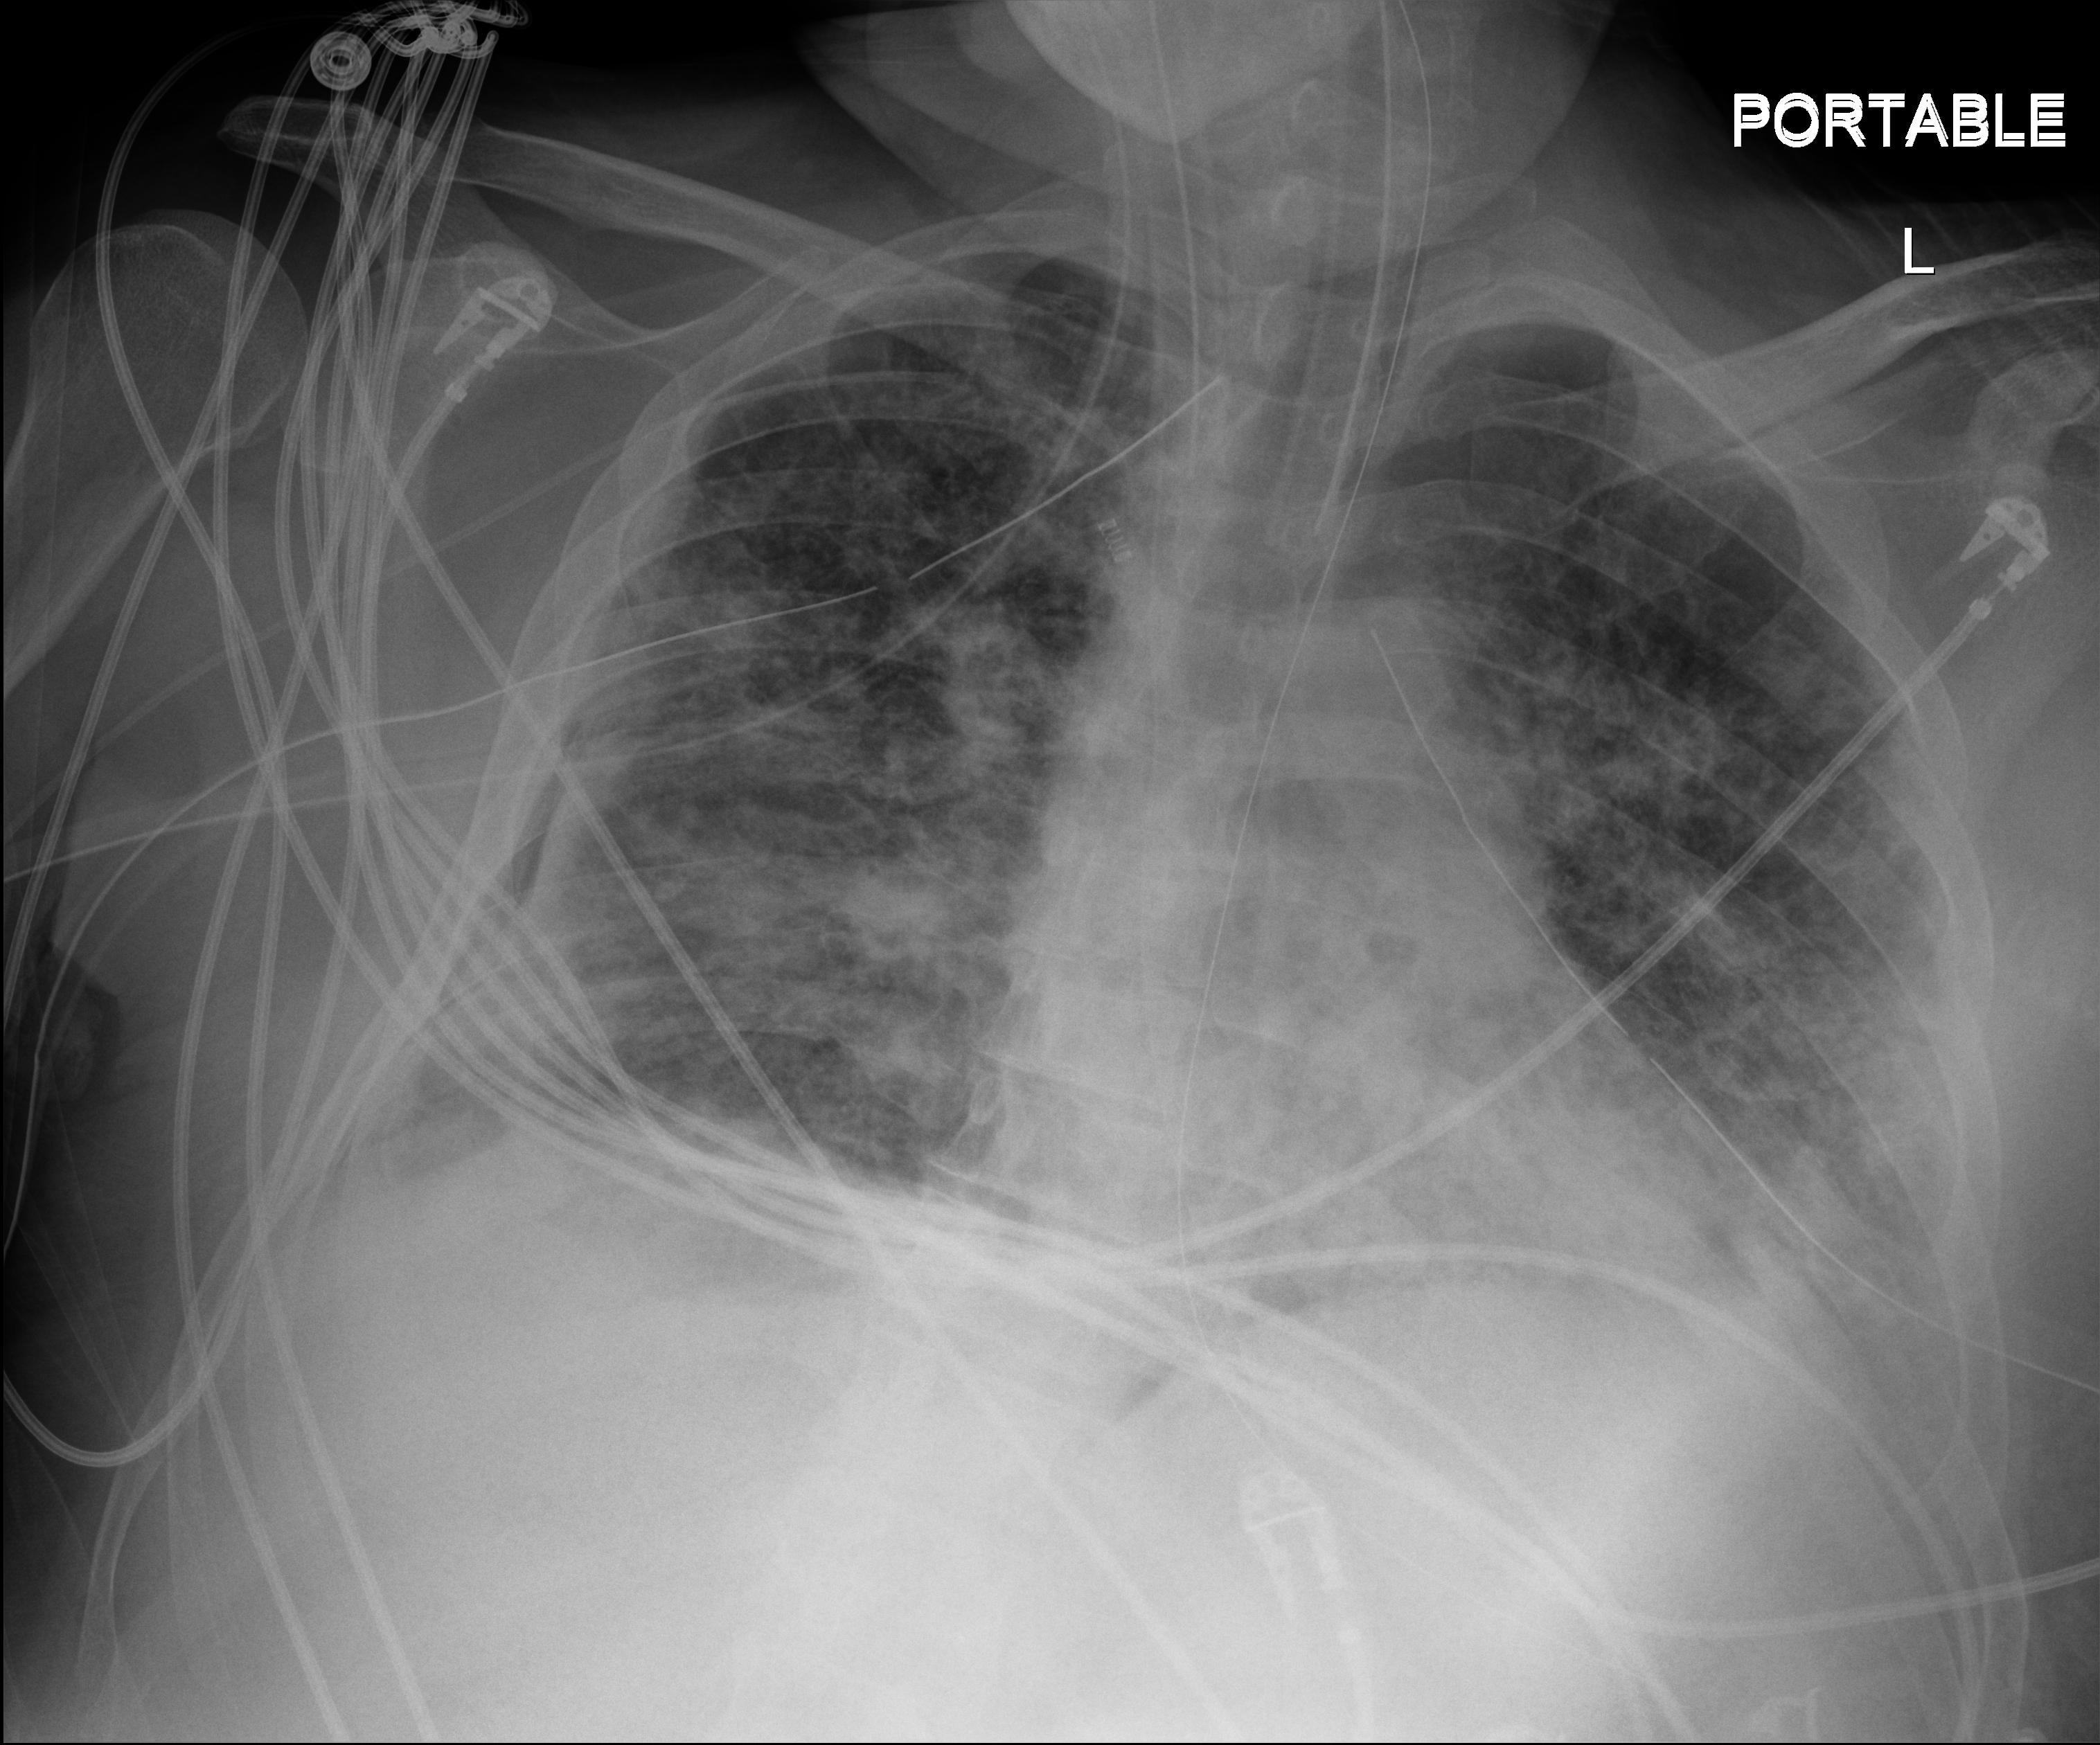
Portable chest radiograph. Patient hospitalised with COVID-19; male, aged 18–59 years.
Hospital-stay facts (about this admission, not read from this image; timing relative to this image not recorded): diabetes (admission record): yes; admitted to intensive care during this hospital stay: yes; mechanically ventilated during this hospital stay: yes.